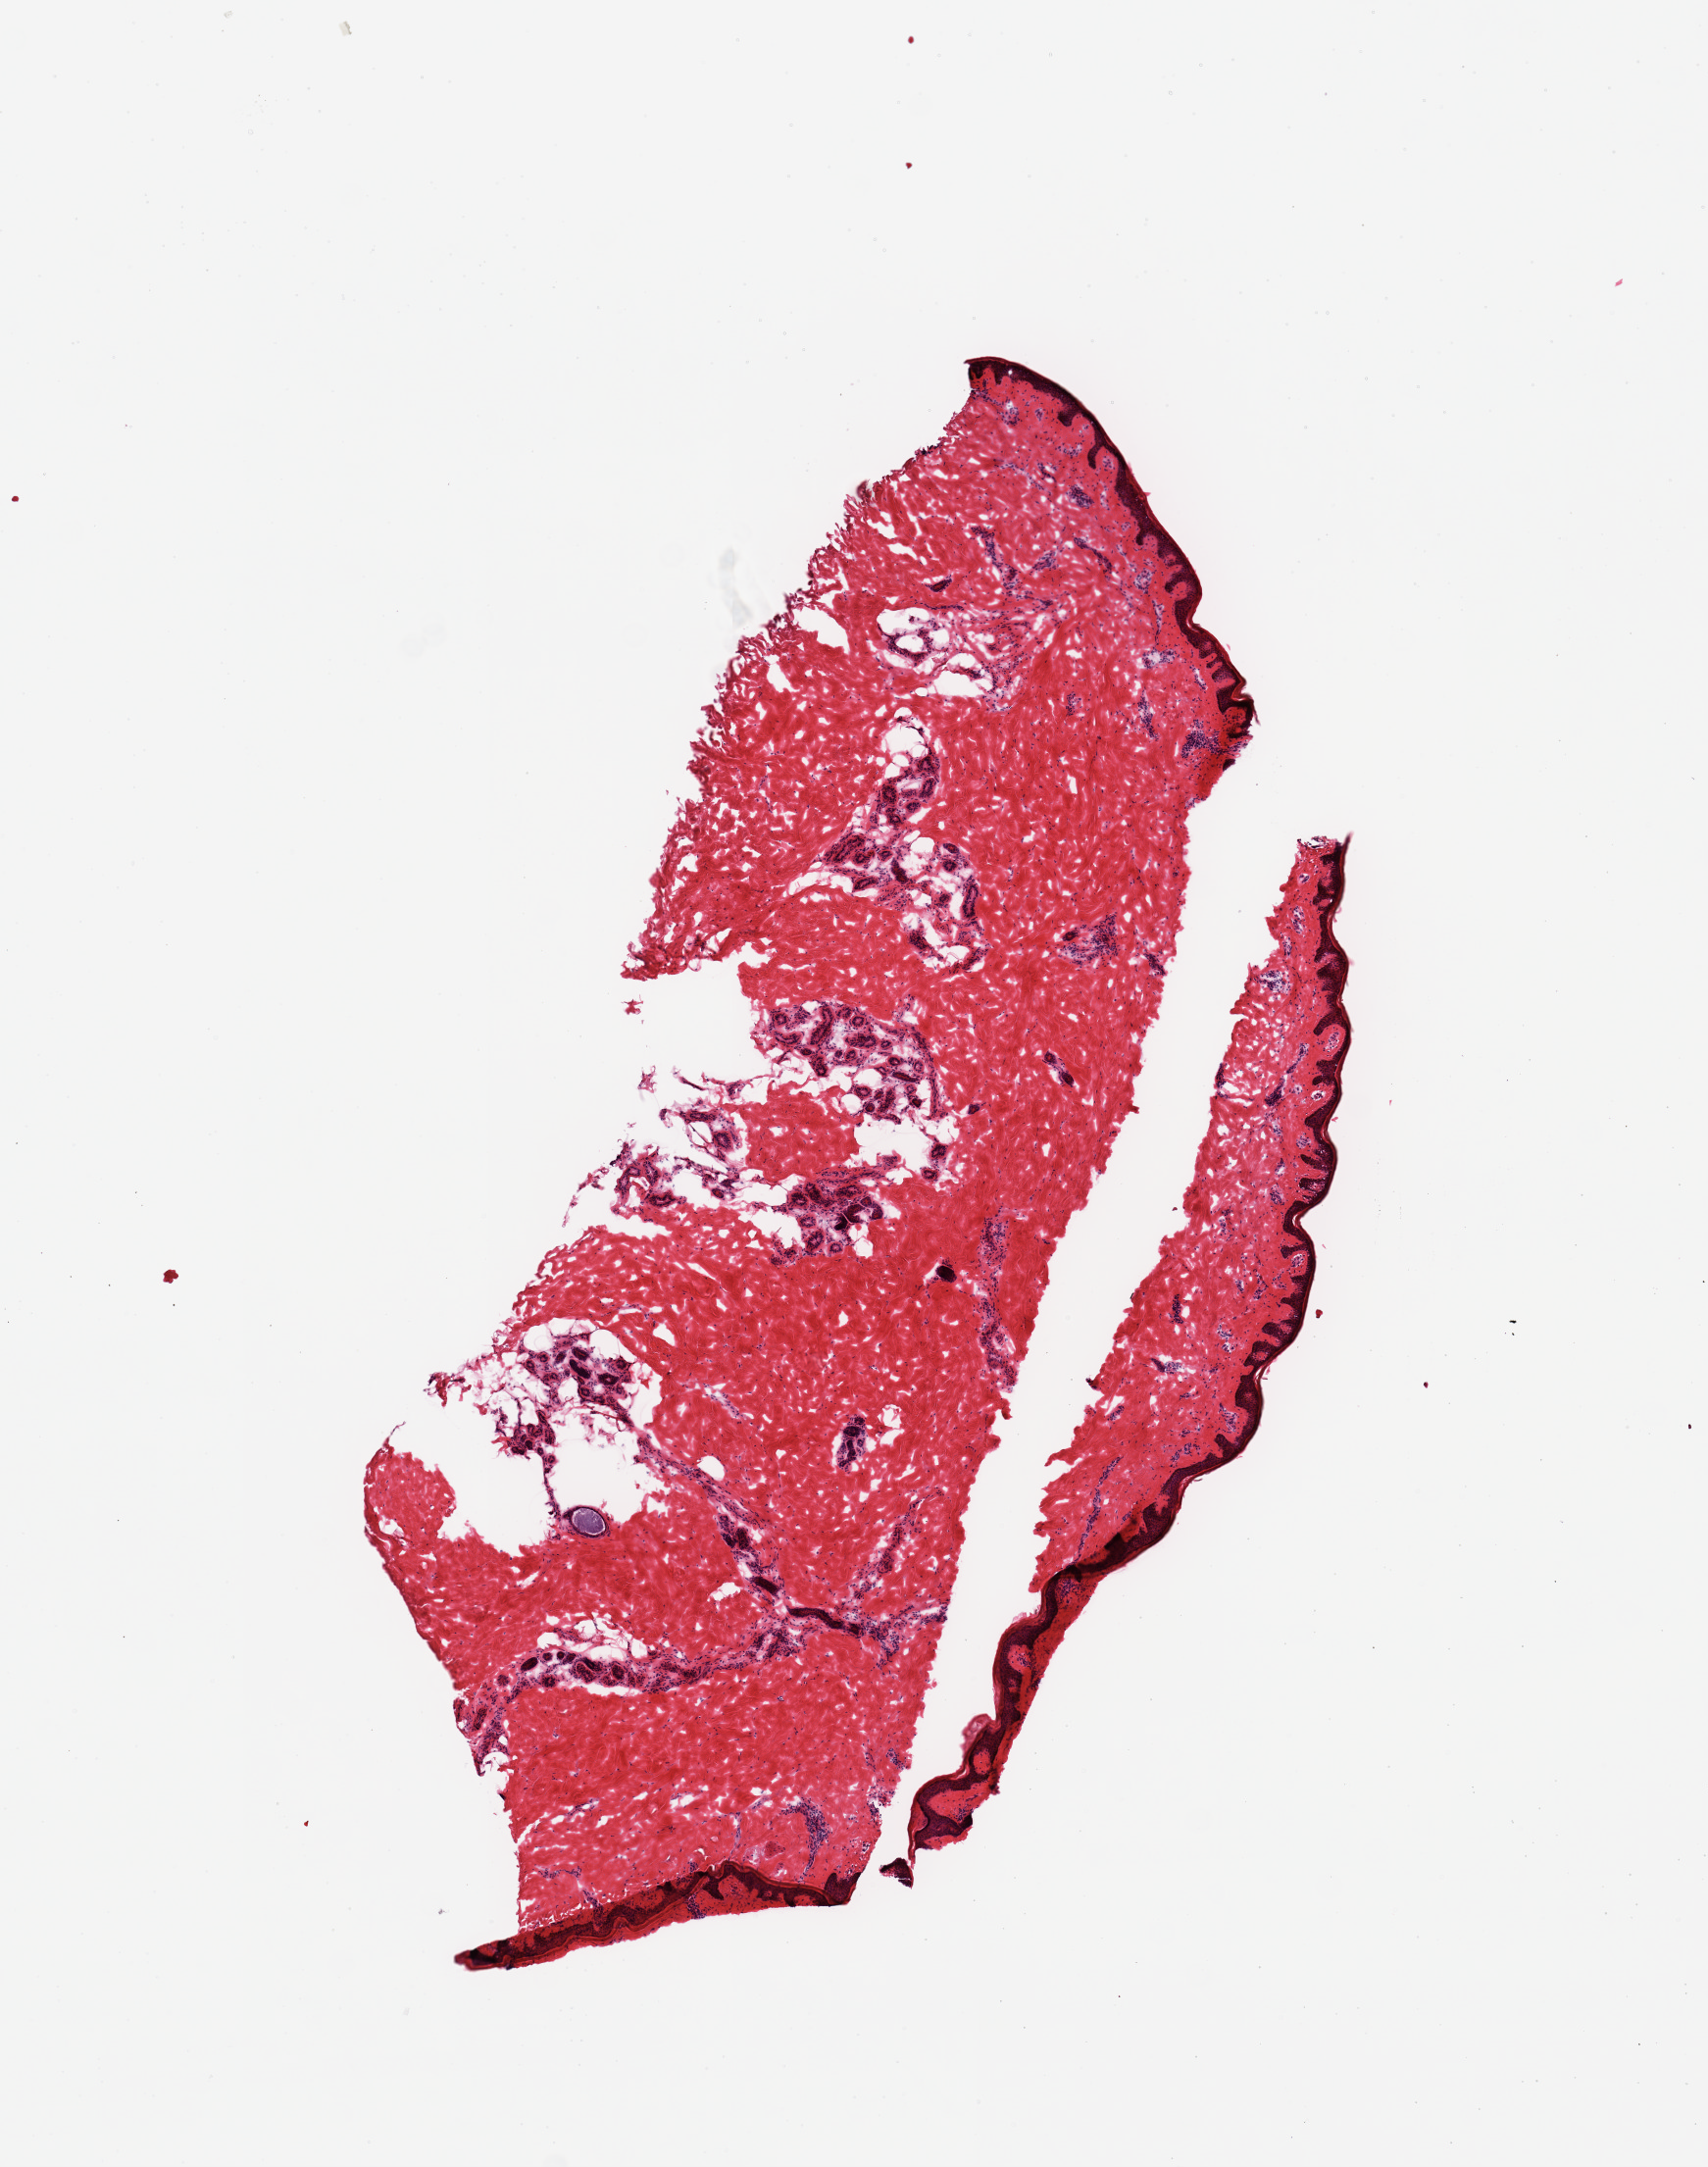
Whole-slide image, hematoxylin and eosin (H&E) stain, a low-resolution overview of the entire scanned area, about 6.9 x 8.7 mm (acquisition: 20x scan); frozen section; sampled site (target tissue): skin of lower leg; tissue donor sample. Donor: male.
Review note (as recorded): 1 piece (fragmented).